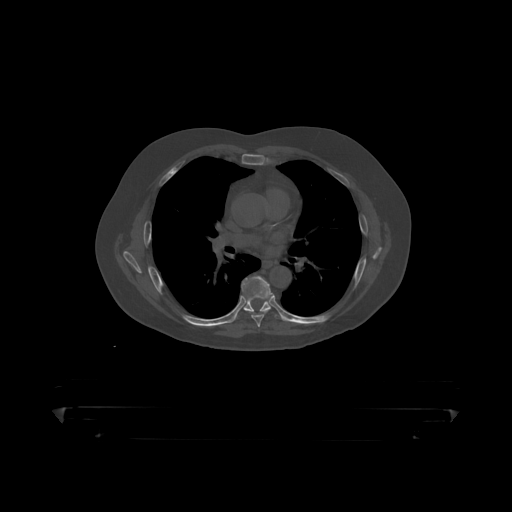
CT including the spine, one axial slice. Slice 290 of 390 in the series (ordered by position). Reconstruction kernel STANDARD. 120 kVp. Bone window (W 1800 / L 400 HU). 512 × 512 image matrix, field of view 650 × 650 mm. Male patient, age 60 years. Case-level facts recorded for this patient, not image findings: primary cancer: prostate.
Structures marked on this image (semi-automatic segmentation, software-assisted and operator-edited):
- T6 vertebra: bounding box (x1, y1, x2, y2) in pixels: (242, 277, 272, 319)
- T7 vertebra: (243, 292, 278, 316)